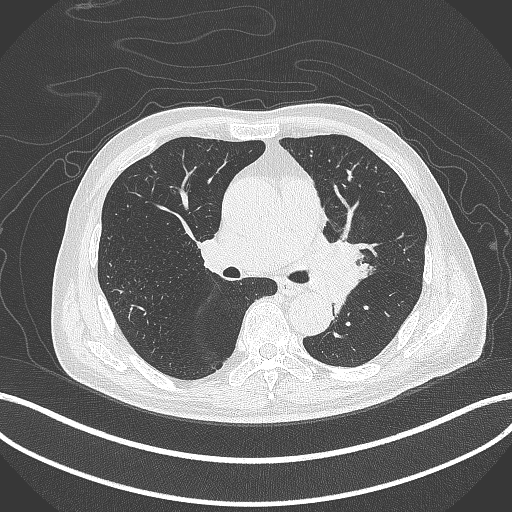
Chest CT, one axial slice; slice 251 of 417 in the series (ordered by position); 120 kVp; lung window (W 1500 / L -600 HU); 512 × 512 image matrix, field of view 400 × 400 mm. Patient: male, 77 years. Case-level facts recorded for this patient, not image findings: clinical TNM (as recorded): T3 N1 M0.
Outlined on this slice (rectangle marked by the reading radiologist):
- lung tumour (recorded histology: adenocarcinoma): box from (x=305, y=229) to (x=371, y=306) px